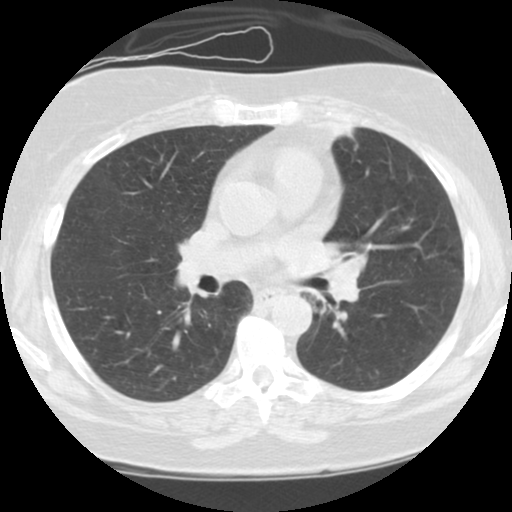
Low-dose screening chest CT, one axial slice; slice 61 of 108 in the series (ordered by position); 120 kVp; lung window (W 1500 / L -600 HU); 2.5 mm slice thickness; 512 × 512 image matrix, field of view 300 × 300 mm.
Annotated regions visible in this slice (expert manual segmentation):
- lesion 1 (tumor, hilum of left lung): bounding box [x1, y1, x2, y2] px = [325, 257, 366, 303]